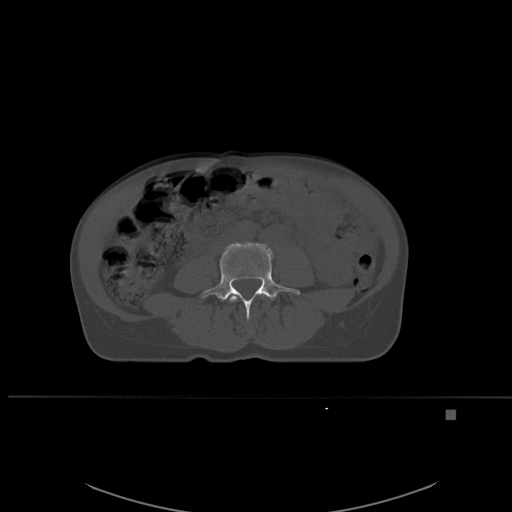
CT including the spine, one axial slice. Slice 196 of 537 in the series (ordered by position). Bone window (W 1800 / L 400 HU). 1.5 mm slice thickness. 512 × 512 image matrix, field of view 440 × 440 mm. Patient: female, 45 years. Case-level facts recorded for this patient, not image findings: primary cancer: lung.
Annotated regions visible in this slice (semi-automatically segmented with operator editing):
- L3 vertebra: box from (x=229, y=293) to (x=268, y=302) px
- L4 vertebra: (x=201, y=242)–(x=300, y=320)